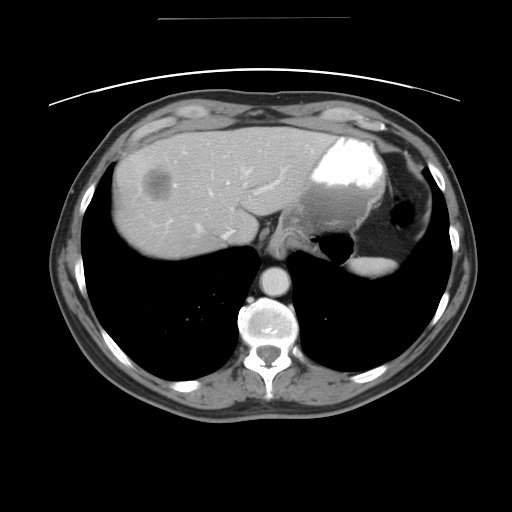
Contrast-enhanced abdominal CT, one axial slice. Position 39 of 49 along the scan axis. Reconstruction kernel STANDARD. Soft-tissue window (W 400 / L 40 HU). 5 mm slice thickness. 512 × 512 image matrix. Male patient, age 57 years. From the clinical record (not read from this slice): diagnosis: colorectal cancer liver metastases, imaged before liver resection; multiple liver metastases: yes; largest metastasis: 4 cm; disease in both lobes: no.
Annotated regions visible in this slice (manually delineated by an expert):
- hepatic veins: box from (x=195, y=169) to (x=248, y=229) px
- liver: (x=114, y=126)–(x=334, y=258)
- planned liver remnant (the part of the liver to remain after resection): (x=205, y=126)–(x=334, y=243)
- portal vein (with intrahepatic branches): (x=173, y=151)–(x=278, y=193)
- liver metastasis: (x=139, y=167)–(x=176, y=203)